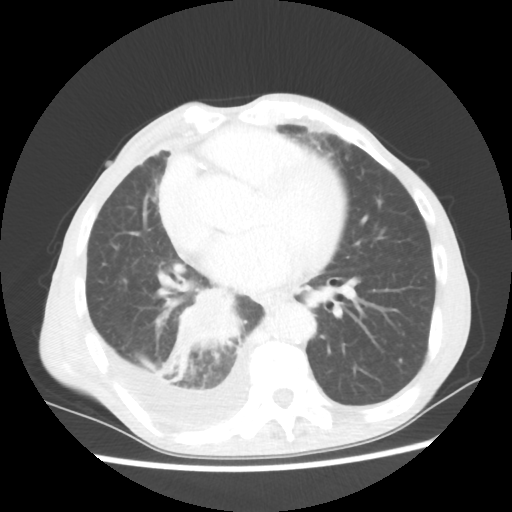
Chest CT, one axial slice. Position 26 of 60 along the scan axis. Reconstruction kernel STANDARD. Lung window (W 1500 / L -600 HU). 5 mm slice thickness. 512 × 512 image matrix. Patient: male, 76 years. From the clinical record (not read from this slice): clinical TNM (as recorded): T3 N3 M1a; histopathological grade: G3.
Annotated regions visible in this slice (rectangle marked by the reading radiologist):
- lung tumour (recorded histology: squamous cell carcinoma): bounding box <155,284,249,389> (left, top, right, bottom; pixels)